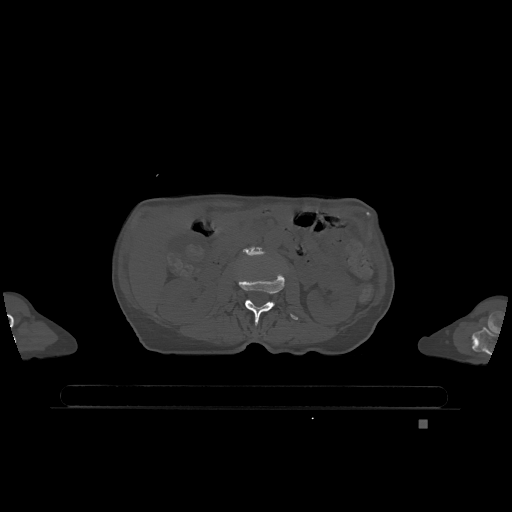
CT including the spine, one axial slice; slice 406 of 1317 in the series (ordered by position); bone window (W 1800 / L 400 HU); 0.5 mm slice thickness; 512 × 512 image matrix, field of view 500 × 500 mm. Female patient, age 74 years. From the clinical record (not read from this slice): primary cancer: lung; vertebrae with lytic lesions (as recorded): T1, T4, T5, T6, L4, L5.
Outlined on this slice (semi-automatically segmented with operator editing):
- L2 vertebra: bounding box (x1, y1, x2, y2) in pixels: (238, 273, 298, 325)
- L3 vertebra: (244, 246, 264, 256)